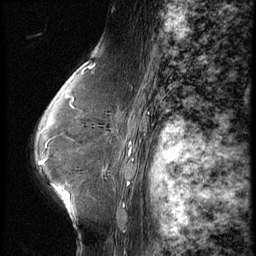
Breast MRI (dynamic contrast-enhanced), one sagittal slice; position 43 of 62 along the scan axis; 3 images stored at this slice position (order not interpretable as contrast timing); 1.5 T; TE 4.2 ms, TR 9 ms; 2.5 mm slice thickness; 256 × 256 image matrix, field of view 180 × 180 mm. Patient: female, 65 years. Case-level facts recorded for this patient, not image findings: setting: breast cancer imaged before/during neoadjuvant chemotherapy; receptor status: HR-positive, HER2-negative.
Annotated regions visible in this slice (semi-automatic segmentation, software-assisted and operator-edited):
- analysis volume of interest (the breast-tissue region the enhancement analysis was run in; not a lesion): bounding box [x1, y1, x2, y2] px = [104, 104, 154, 161]
- tumour enhancement mask (voxels above the 140 % enhancement threshold inside the analysis volume of interest): [130, 143, 132, 152]